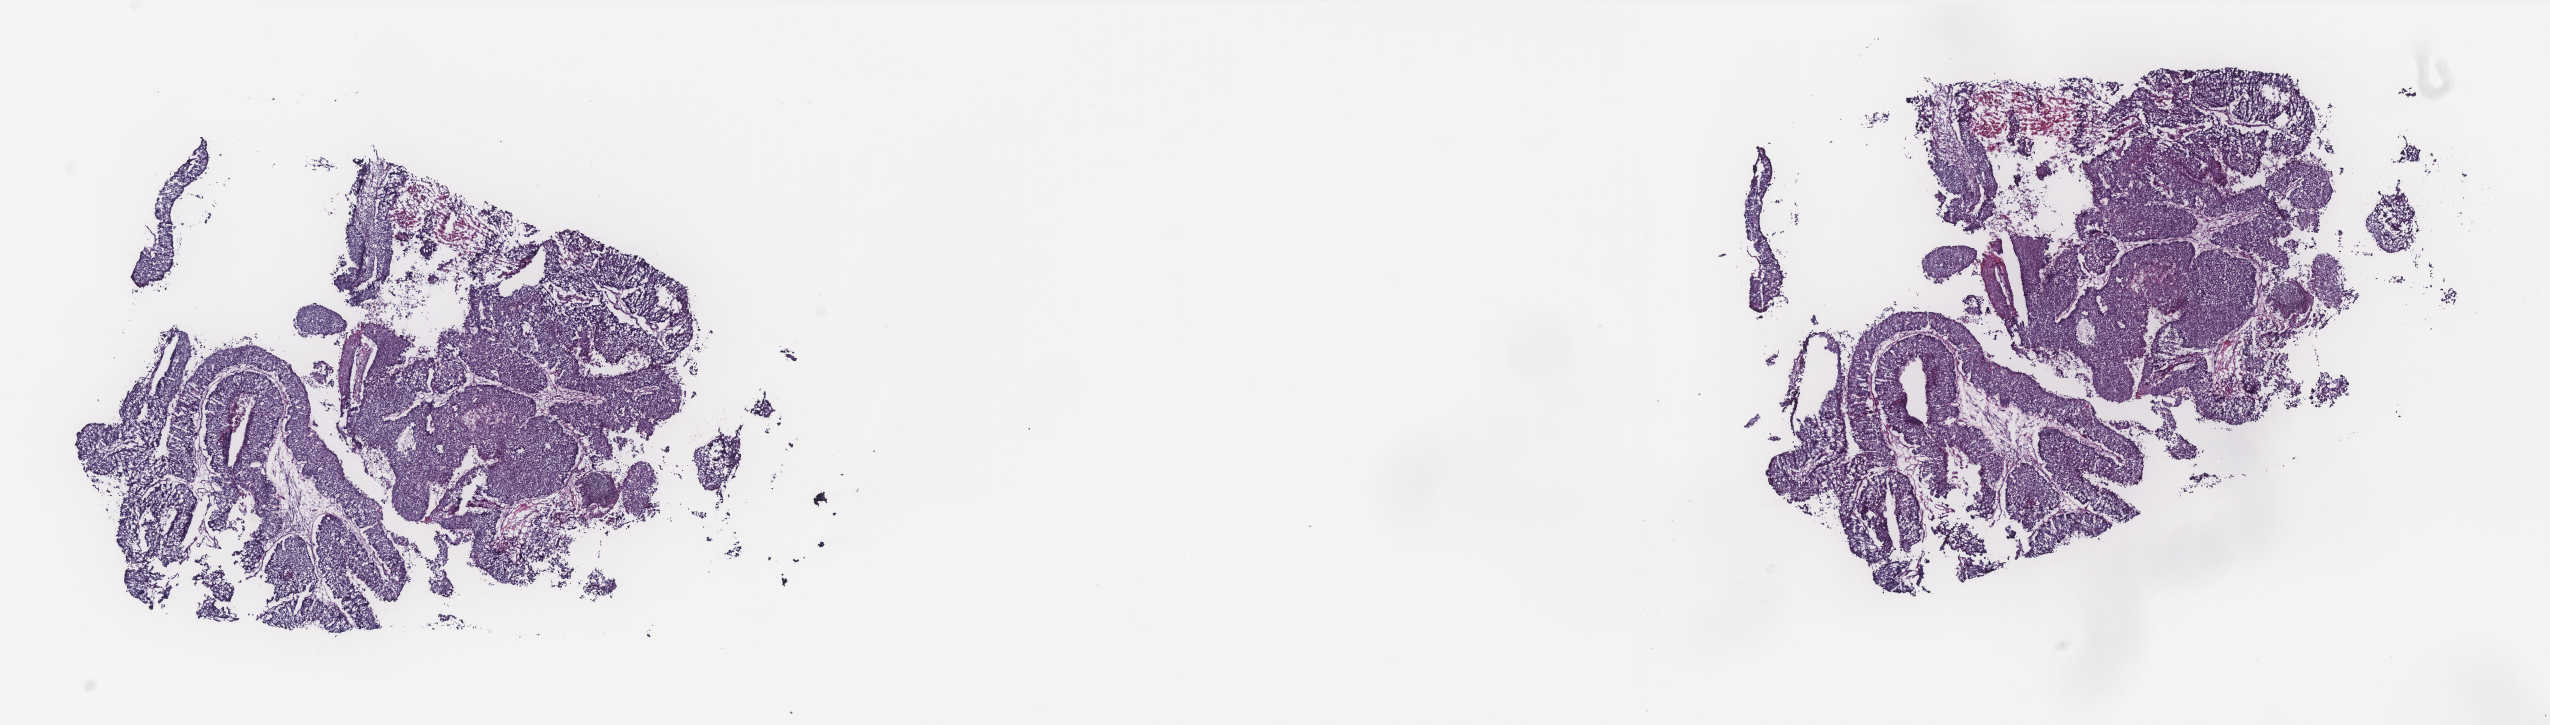
Hematoxylin and eosin (H&E) stained whole-slide image, a low-resolution overview of the entire scanned area, about 20.4 x 5.8 mm; frozen section; primary tumour sample from the uterus. Female patient; age at initial diagnosis 55 years. Histologic grade: G3 (poorly differentiated). Pathologist review of this section (percent, as recorded): tumour cells 87%, tumour nuclei 90%, normal cells 0%, stromal cells 10%, necrosis 3%. Inflammatory infiltration, as recorded: lymphocyte infiltration 10%, monocyte infiltration 0%, neutrophil infiltration 5%.
Lymph nodes positive (case pathology): 0 of 8 examined. FIGO stage: IA. Histologic diagnosis: Endometrioid adenocarcinoma, NOS.